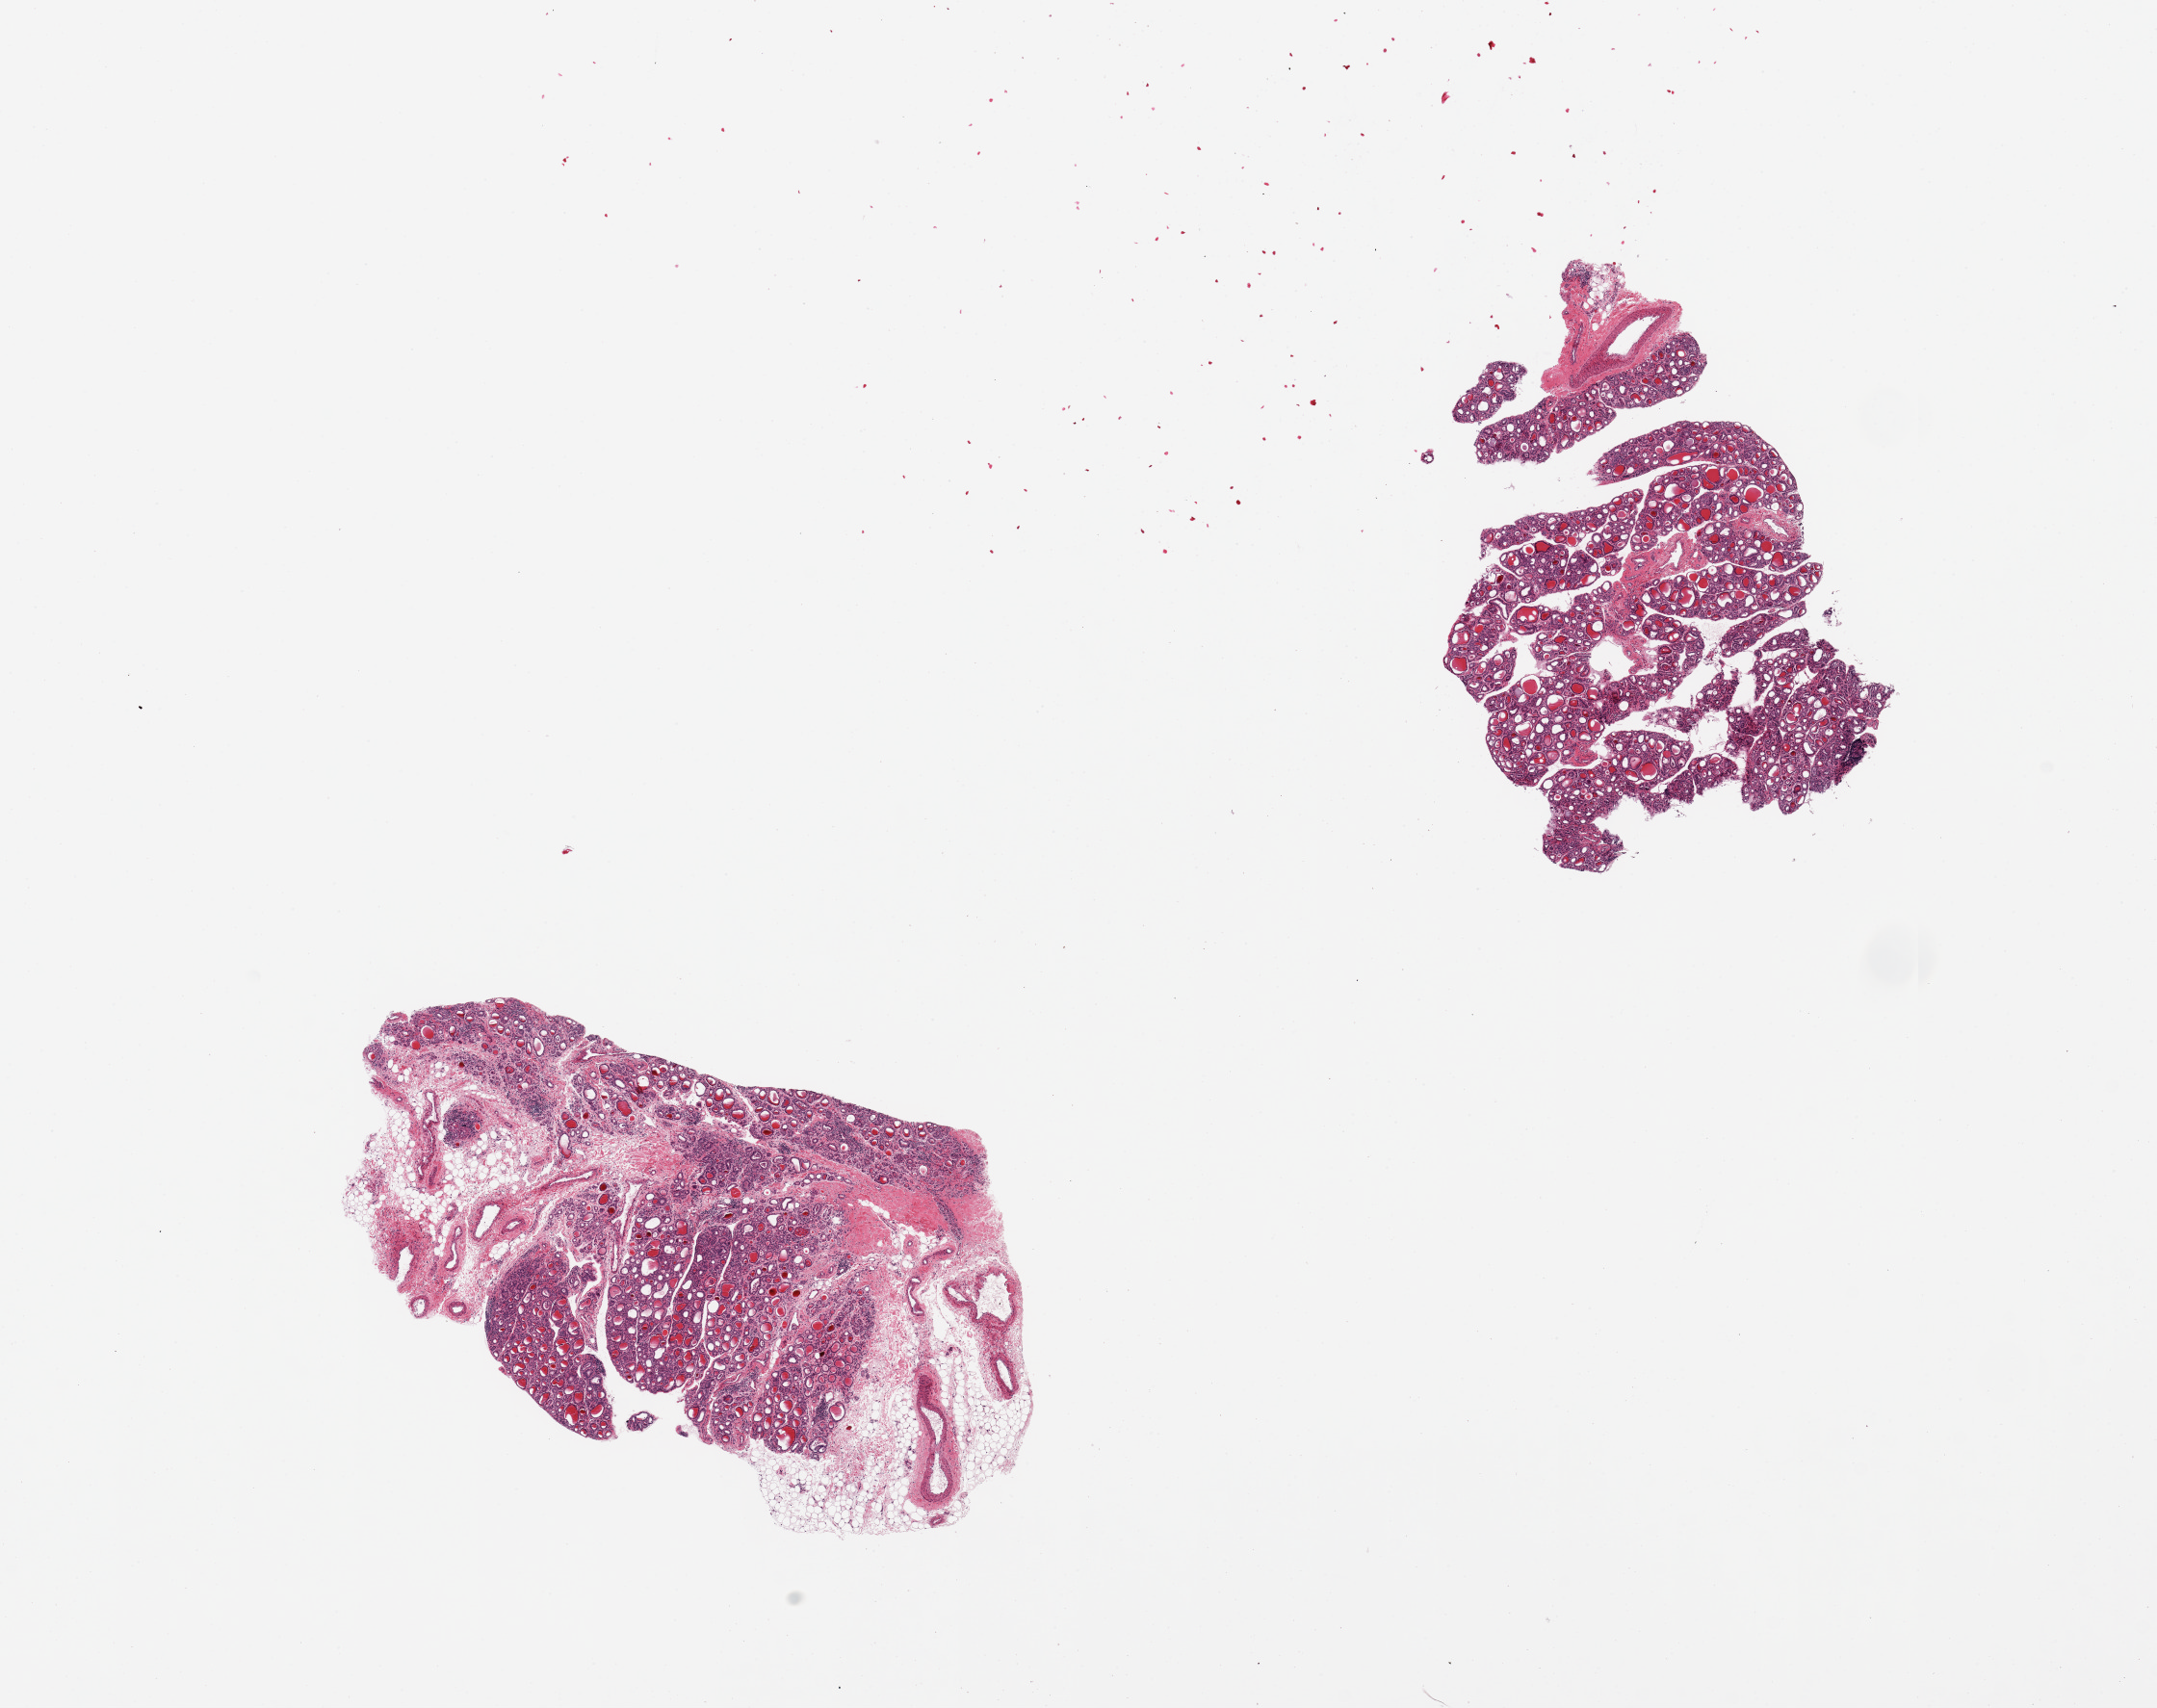
Digitized H&E-stained section, brightfield — a low-resolution overview of the entire scanned area, about 17.7 x 14.0 mm (from a 20x scan), PAXgene-fixed paraffin-embedded (PFPE) section, target tissue: thyroid, tissue donor sample.
Reviewer comment on this tissue sample: 2 pieces, marked atrophy/regressive changes.